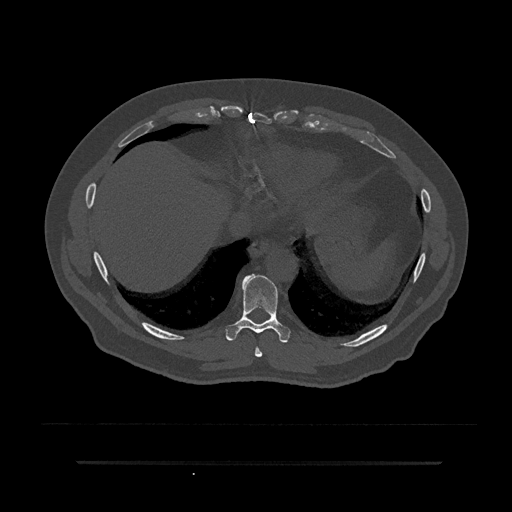
CT including the spine, one axial slice. Slice 379 of 797 in the series (ordered by position). Reconstruction kernel Br40s/3. 120 kVp. Bone window (W 1800 / L 400 HU). 512 × 512 image matrix. Male patient, age 59 years. Case-level facts recorded for this patient, not image findings: primary cancer: bile ducts; vertebrae with lytic lesions (as recorded): T10.
Structures marked on this image (semi-automatic segmentation, software-assisted and operator-edited):
- T8 vertebra: bounding box [x1, y1, x2, y2] px = [255, 347, 263, 357]
- T9 vertebra: [225, 274, 291, 343]